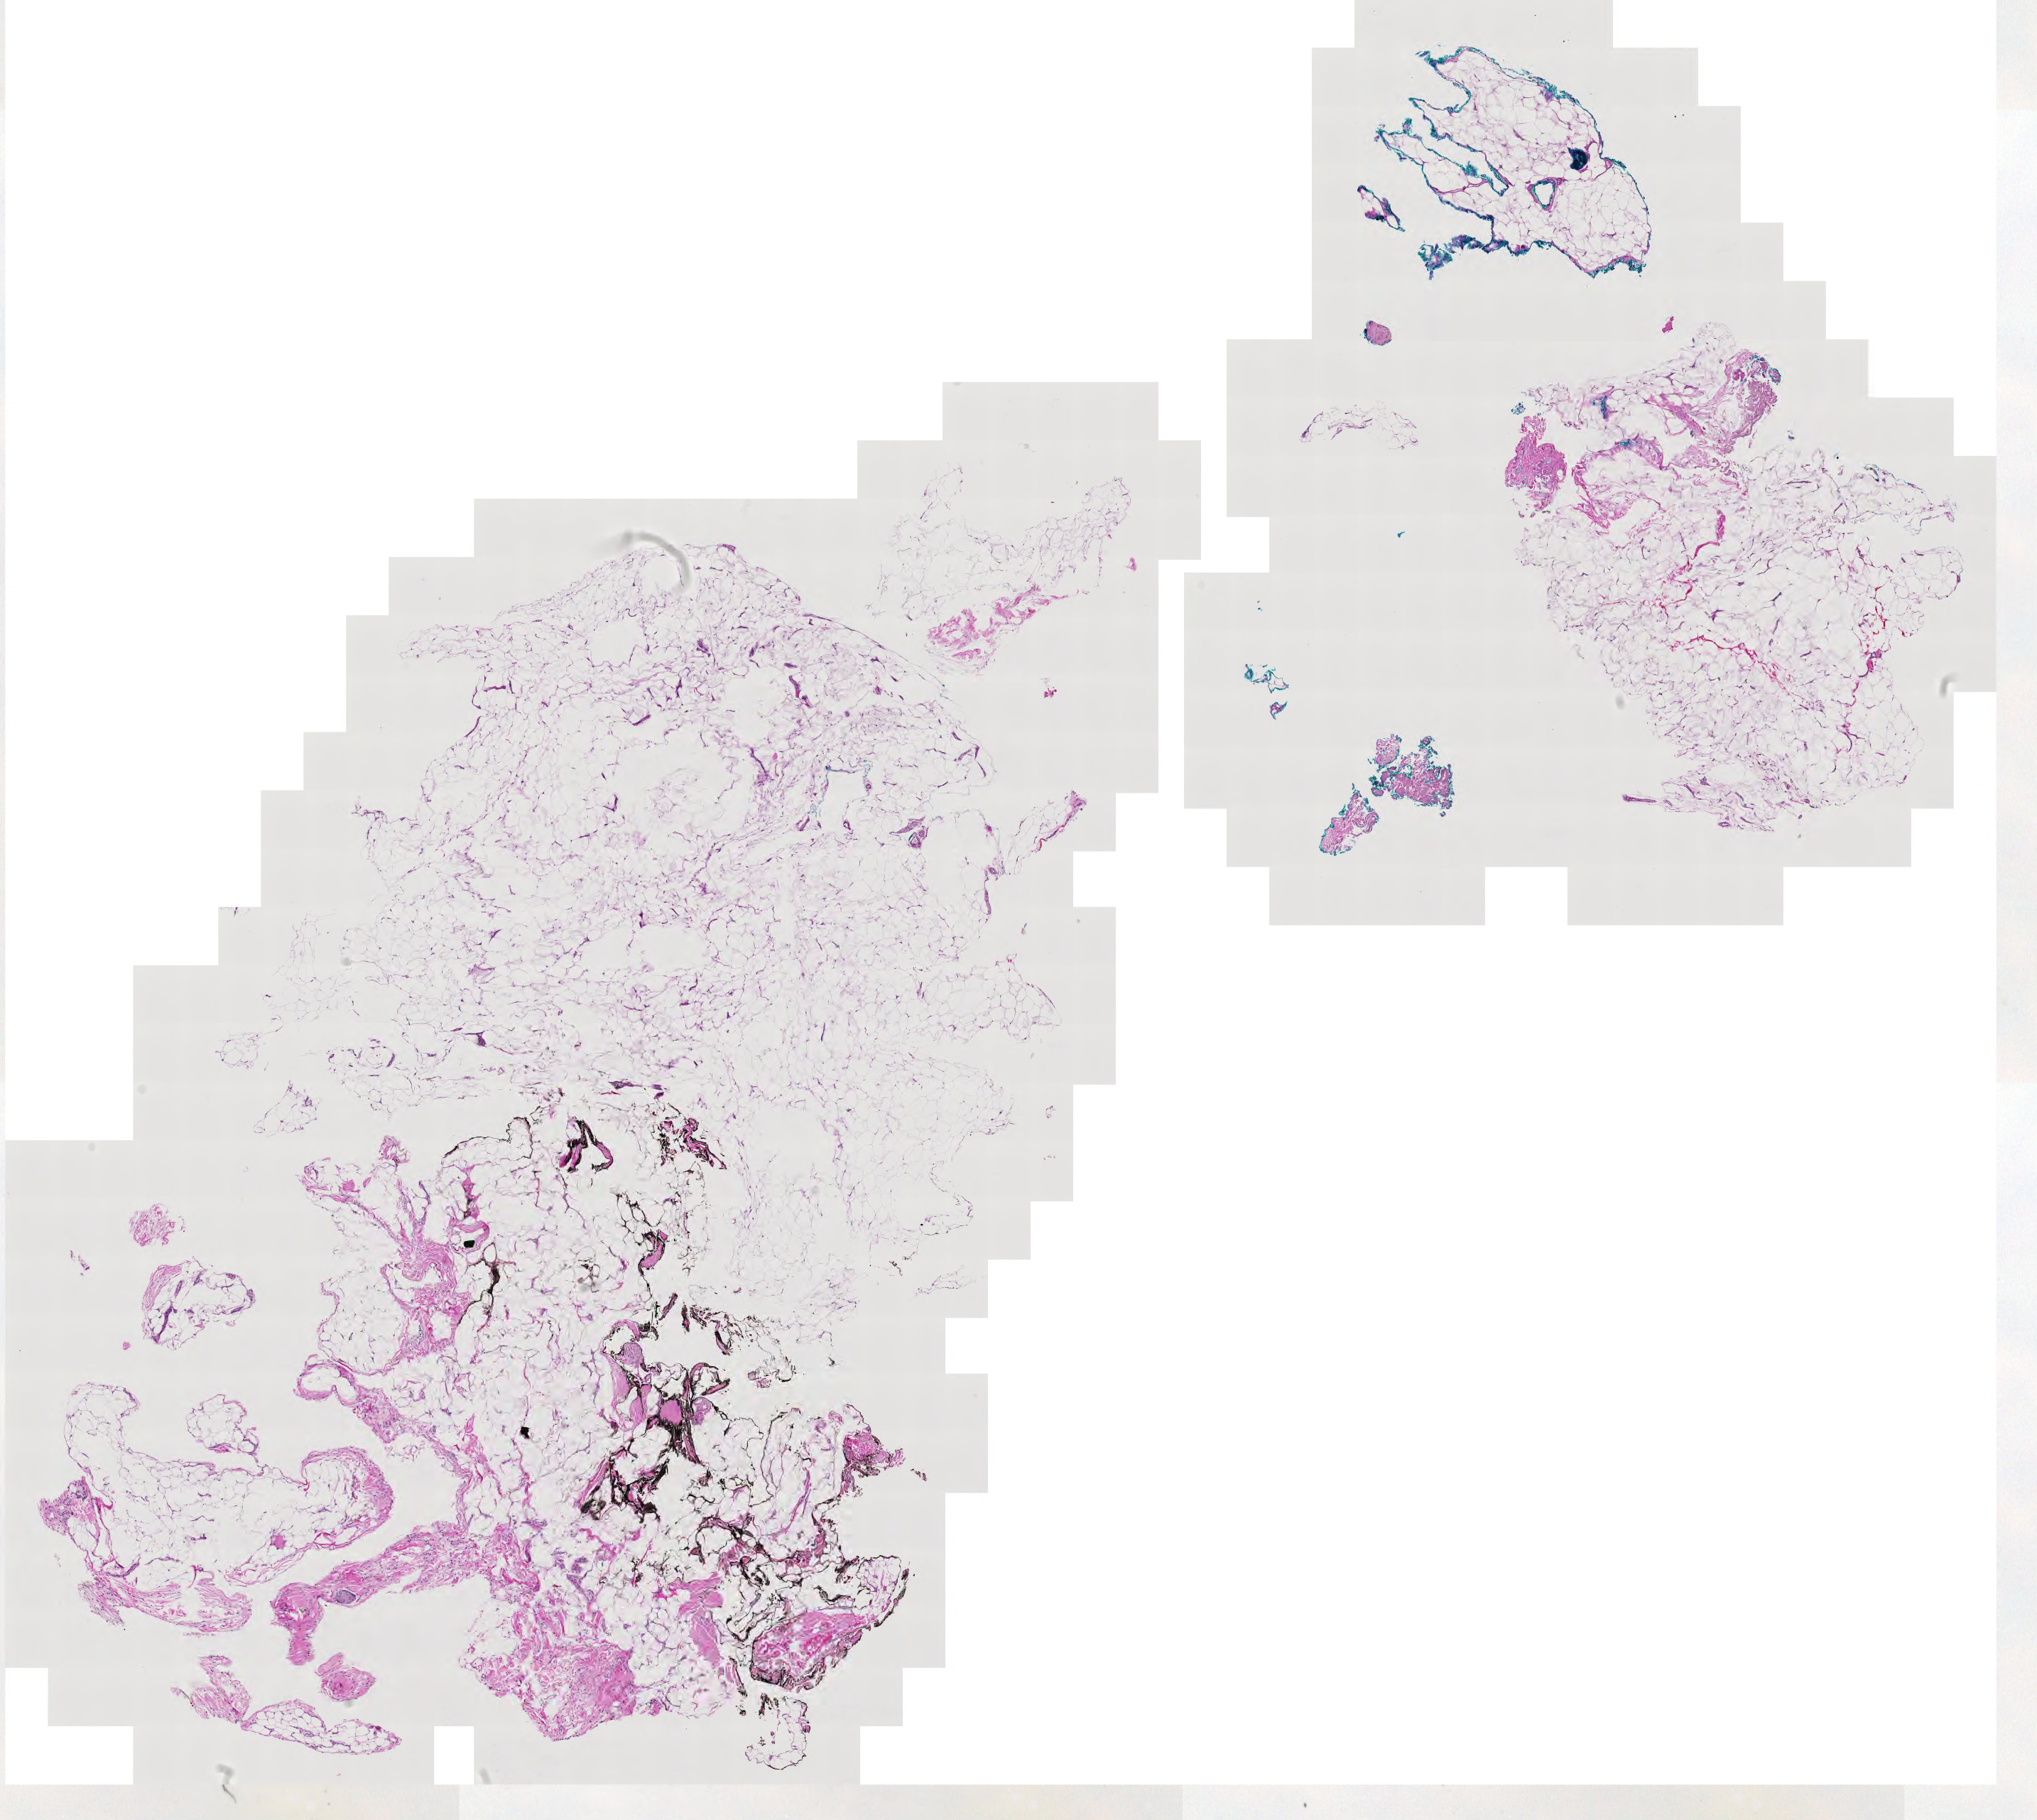
Digitized H&E-stained tissue section (whole slide), low-resolution overview of the scanned area, about 14.8 x 13.2 mm; normal (non-tumour) tissue sample. Patient: male, age 74 years.
• this section: normal (non-tumour) tissue from the same patient
• patient diagnosis (cohort enrolment): sarcoma (site not recorded at cohort level)